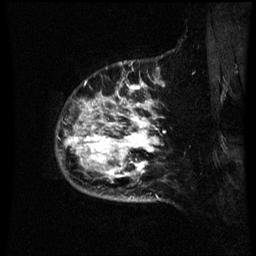
Breast MRI (dynamic contrast-enhanced), one sagittal slice. Slice 57 of 60 in the series (ordered by position). Dynamic contrast-enhanced series, image 2 of 3 at this slice position (ordered by acquisition). 1.5 T. TE 4.2 ms, TR 8.9 ms. 256 × 256 image matrix, field of view 200 × 200 mm. Female patient, age 42 years. Case-level facts recorded for this patient, not image findings: setting: breast cancer imaged before/during neoadjuvant chemotherapy; receptor status: HER2-positive.
Annotated regions visible in this slice (semi-automatic segmentation, software-assisted and operator-edited):
- analysis volume of interest (the breast-tissue region the enhancement analysis was run in; not a lesion): box from (x=66, y=82) to (x=169, y=193) px
- tumour enhancement mask (voxels above the 70 % enhancement threshold inside the analysis volume of interest): (x=66, y=84)–(x=159, y=179)